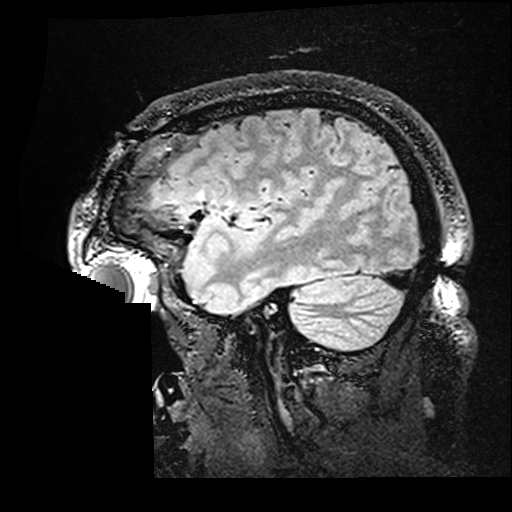
Brain MRI from a brain-tumour surgery series, one sagittal slice. Position 130 of 176 along the scan axis. T2 FLAIR. 1 mm slice thickness. 512 × 512 image matrix, field of view 250 × 250 mm. From the clinical record (not read from this slice): histopathology: Astrocytoma; WHO grade: 2; IDH mutation: yes.
Outlined on this slice (expert manual segmentation):
- residual tumour: bounding box <243,244,253,252> (left, top, right, bottom; pixels)